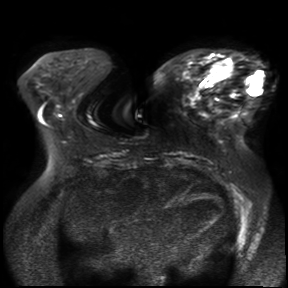
Breast MRI, one axial slice; position 12 of 30 along the scan axis; diffusion-weighted series; image 2 of 4 stored at this slice position (different b-values; order by instance number); 3 T; 4 mm slice thickness; 288 × 288 image matrix, field of view 360 × 360 mm. Female patient.
Outlined on this slice (manually delineated by an expert):
- tumour on diffusion-weighted imaging: bounding box <208,56,233,81> (left, top, right, bottom; pixels)